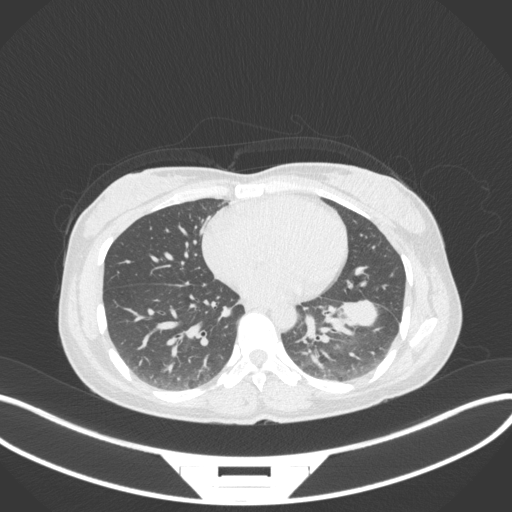
Chest CT, one axial slice. Slice 147 of 361 in the series (ordered by position). Reconstruction kernel B31f. 120 kVp. Lung window (W 1500 / L -600 HU). 1 mm slice thickness. 512 × 512 image matrix. Patient: female, 41 years. From the clinical record (not read from this slice): clinical TNM (as recorded): T2a N3 M1b.
Annotated regions visible in this slice (bounding box drawn by a radiologist):
- lung tumour (recorded histology: adenocarcinoma): bounding box <337,297,386,333> (left, top, right, bottom; pixels)